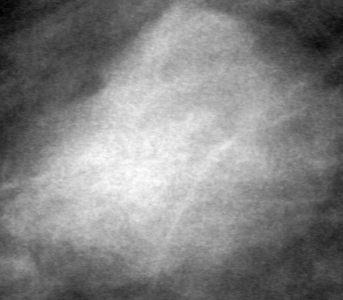
Region of interest cut from a scanned film mammogram (one marked finding), left breast, MLO view.
Marked abnormality: mass, shape lobulated, margins circumscribed; BI-RADS assessment category 4; pathology result (as recorded, not read from the image): benign.